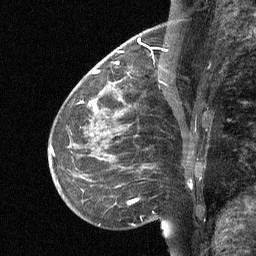
Breast MRI (dynamic contrast-enhanced), one sagittal slice; slice 21 of 64 in the series (ordered by position); dynamic contrast-enhanced study with each time point stored as its own series, time point 2 of 3 at this slice position (early post-contrast, ordered by acquisition time); 1.5 T; TE 4.8 ms, TR 27 ms; 256 × 256 image matrix. Patient: female, 51 years. Case-level facts recorded for this patient, not image findings: setting: breast cancer imaged before/during neoadjuvant chemotherapy; receptor status: HR-positive, HER2-negative.
Annotated regions visible in this slice (semi-automatically segmented with operator editing):
- analysis volume of interest (the breast-tissue region the enhancement analysis was run in; not a lesion): box from (x=112, y=46) to (x=169, y=106) px
- tumour enhancement mask (voxels above the 90 % enhancement threshold inside the analysis volume of interest): (x=115, y=49)–(x=163, y=64)